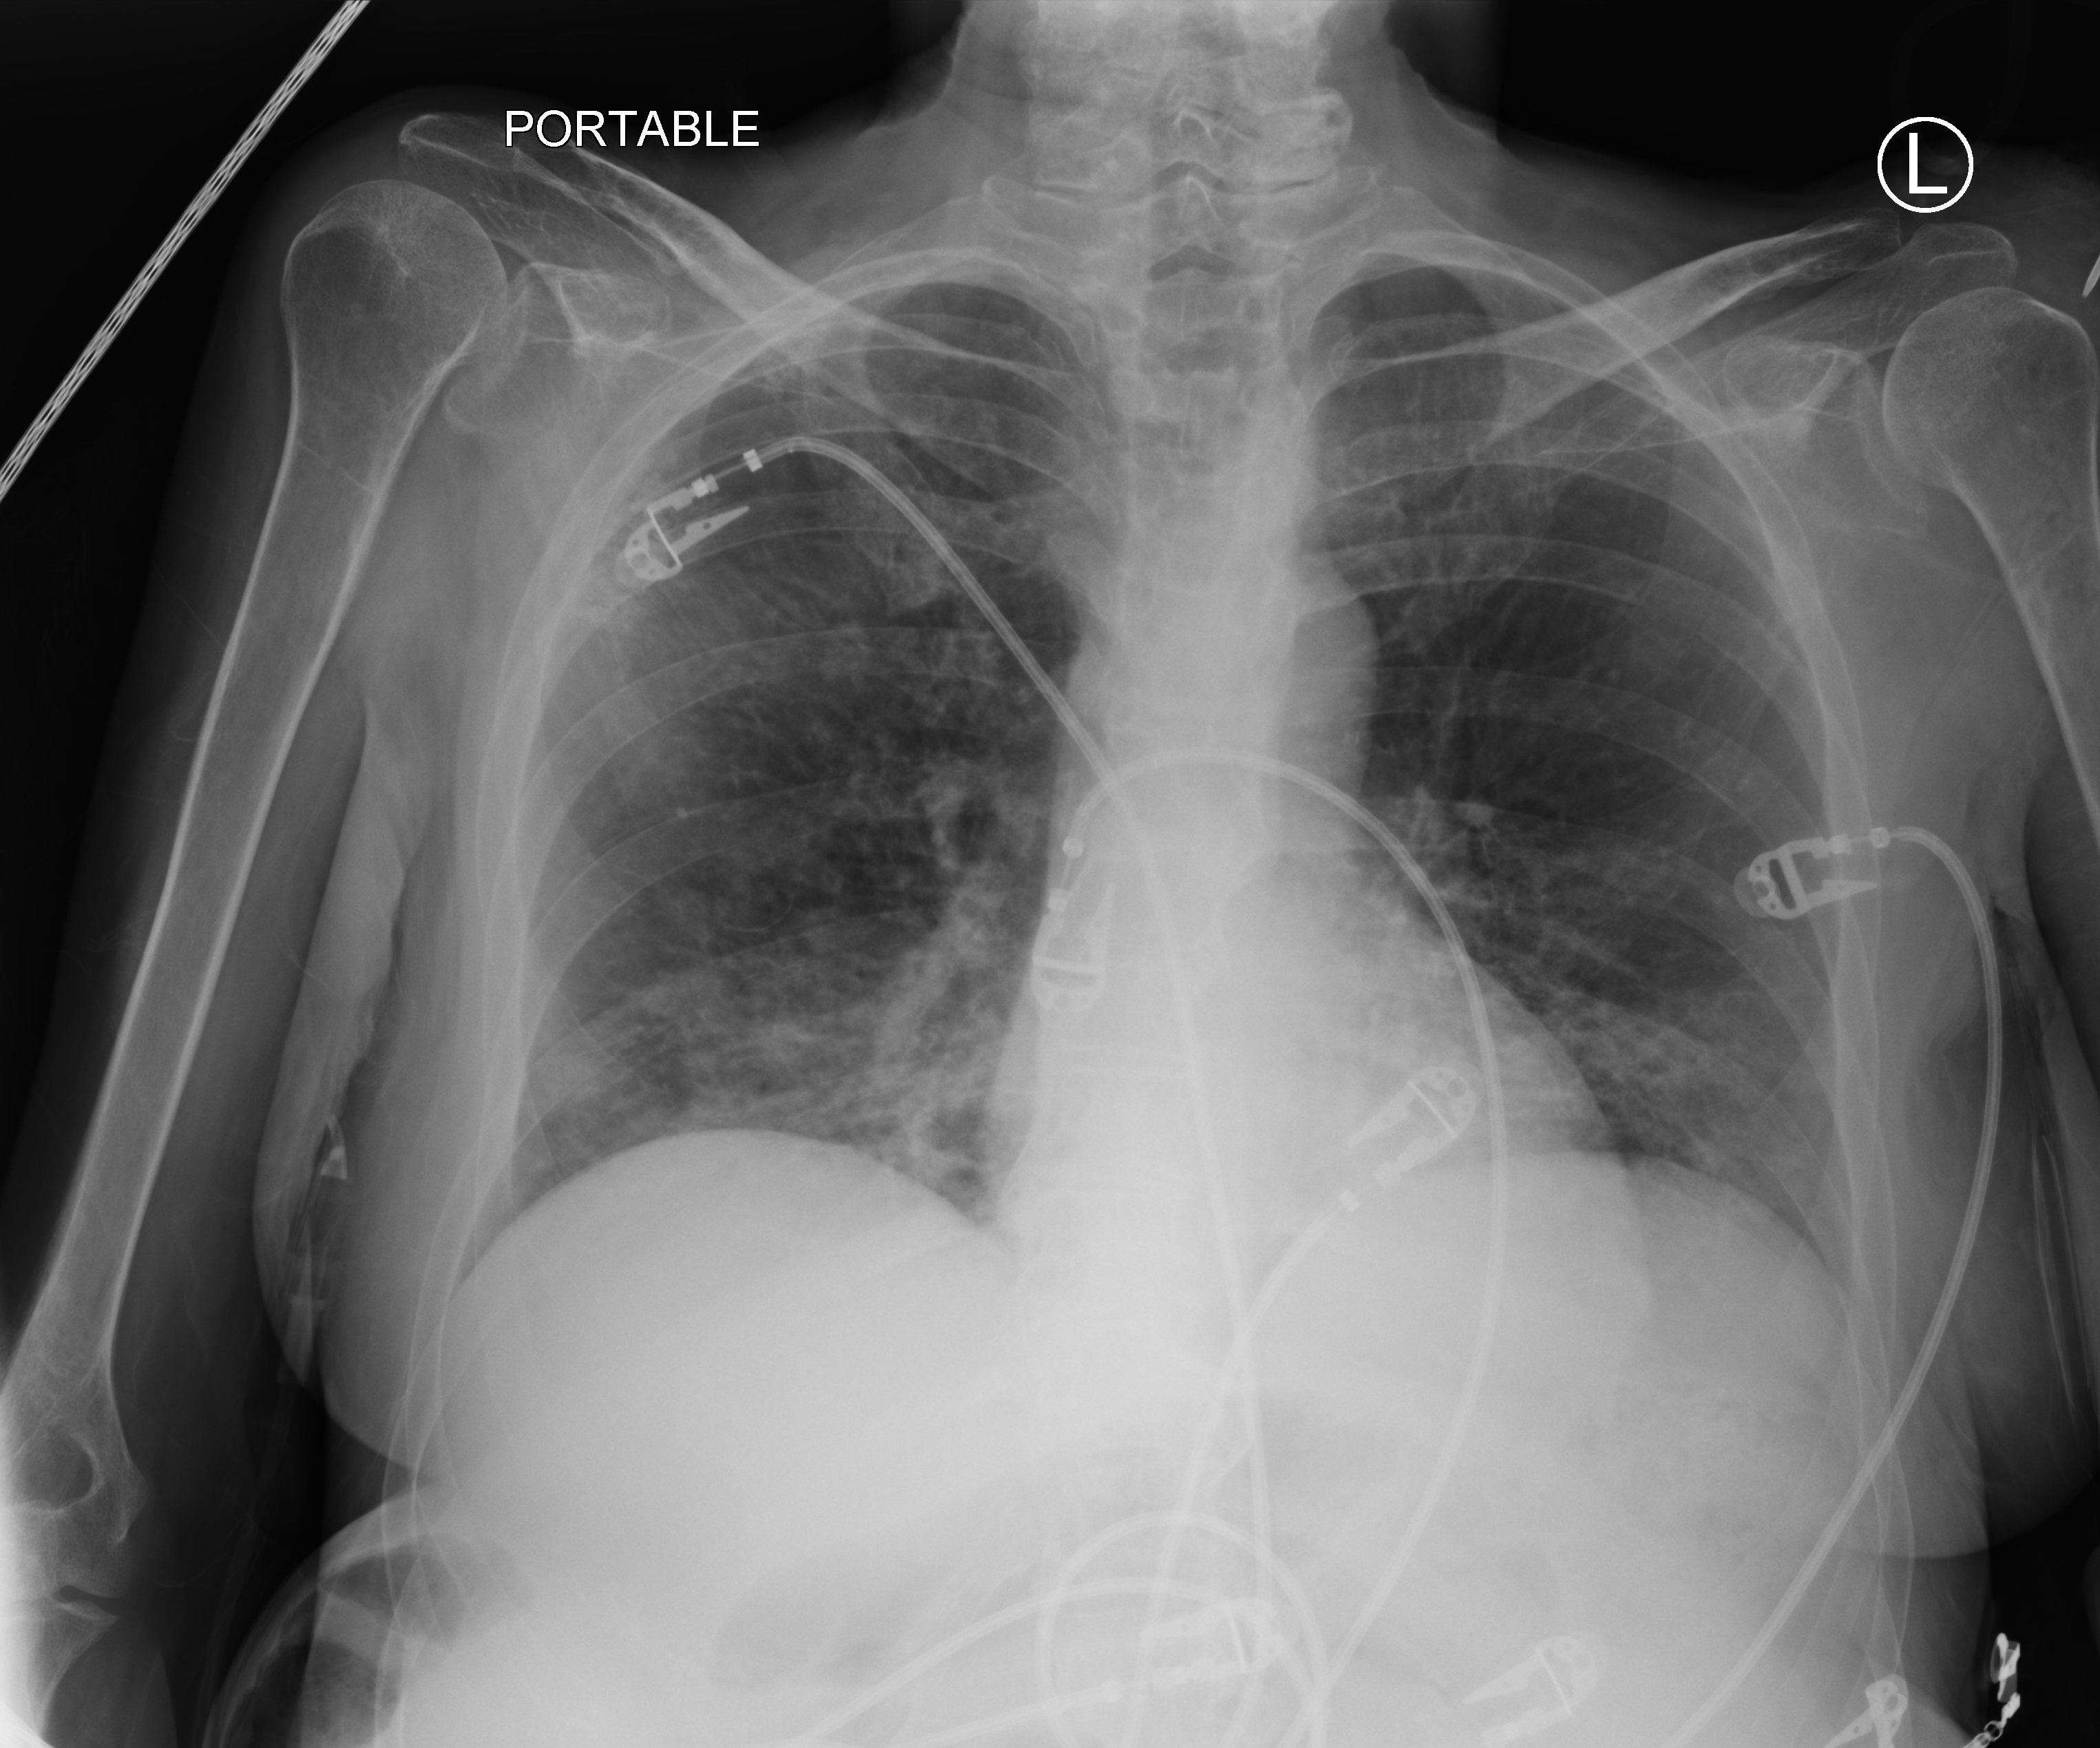
Portable chest radiograph; anteroposterior (AP) projection. Female patient hospitalised with COVID-19, age 60–74 years.
Admission-level facts for this patient (not findings on this image; timing relative to this image not recorded):
- admitted to intensive care during this hospital stay: yes
- mechanically ventilated during this hospital stay: no